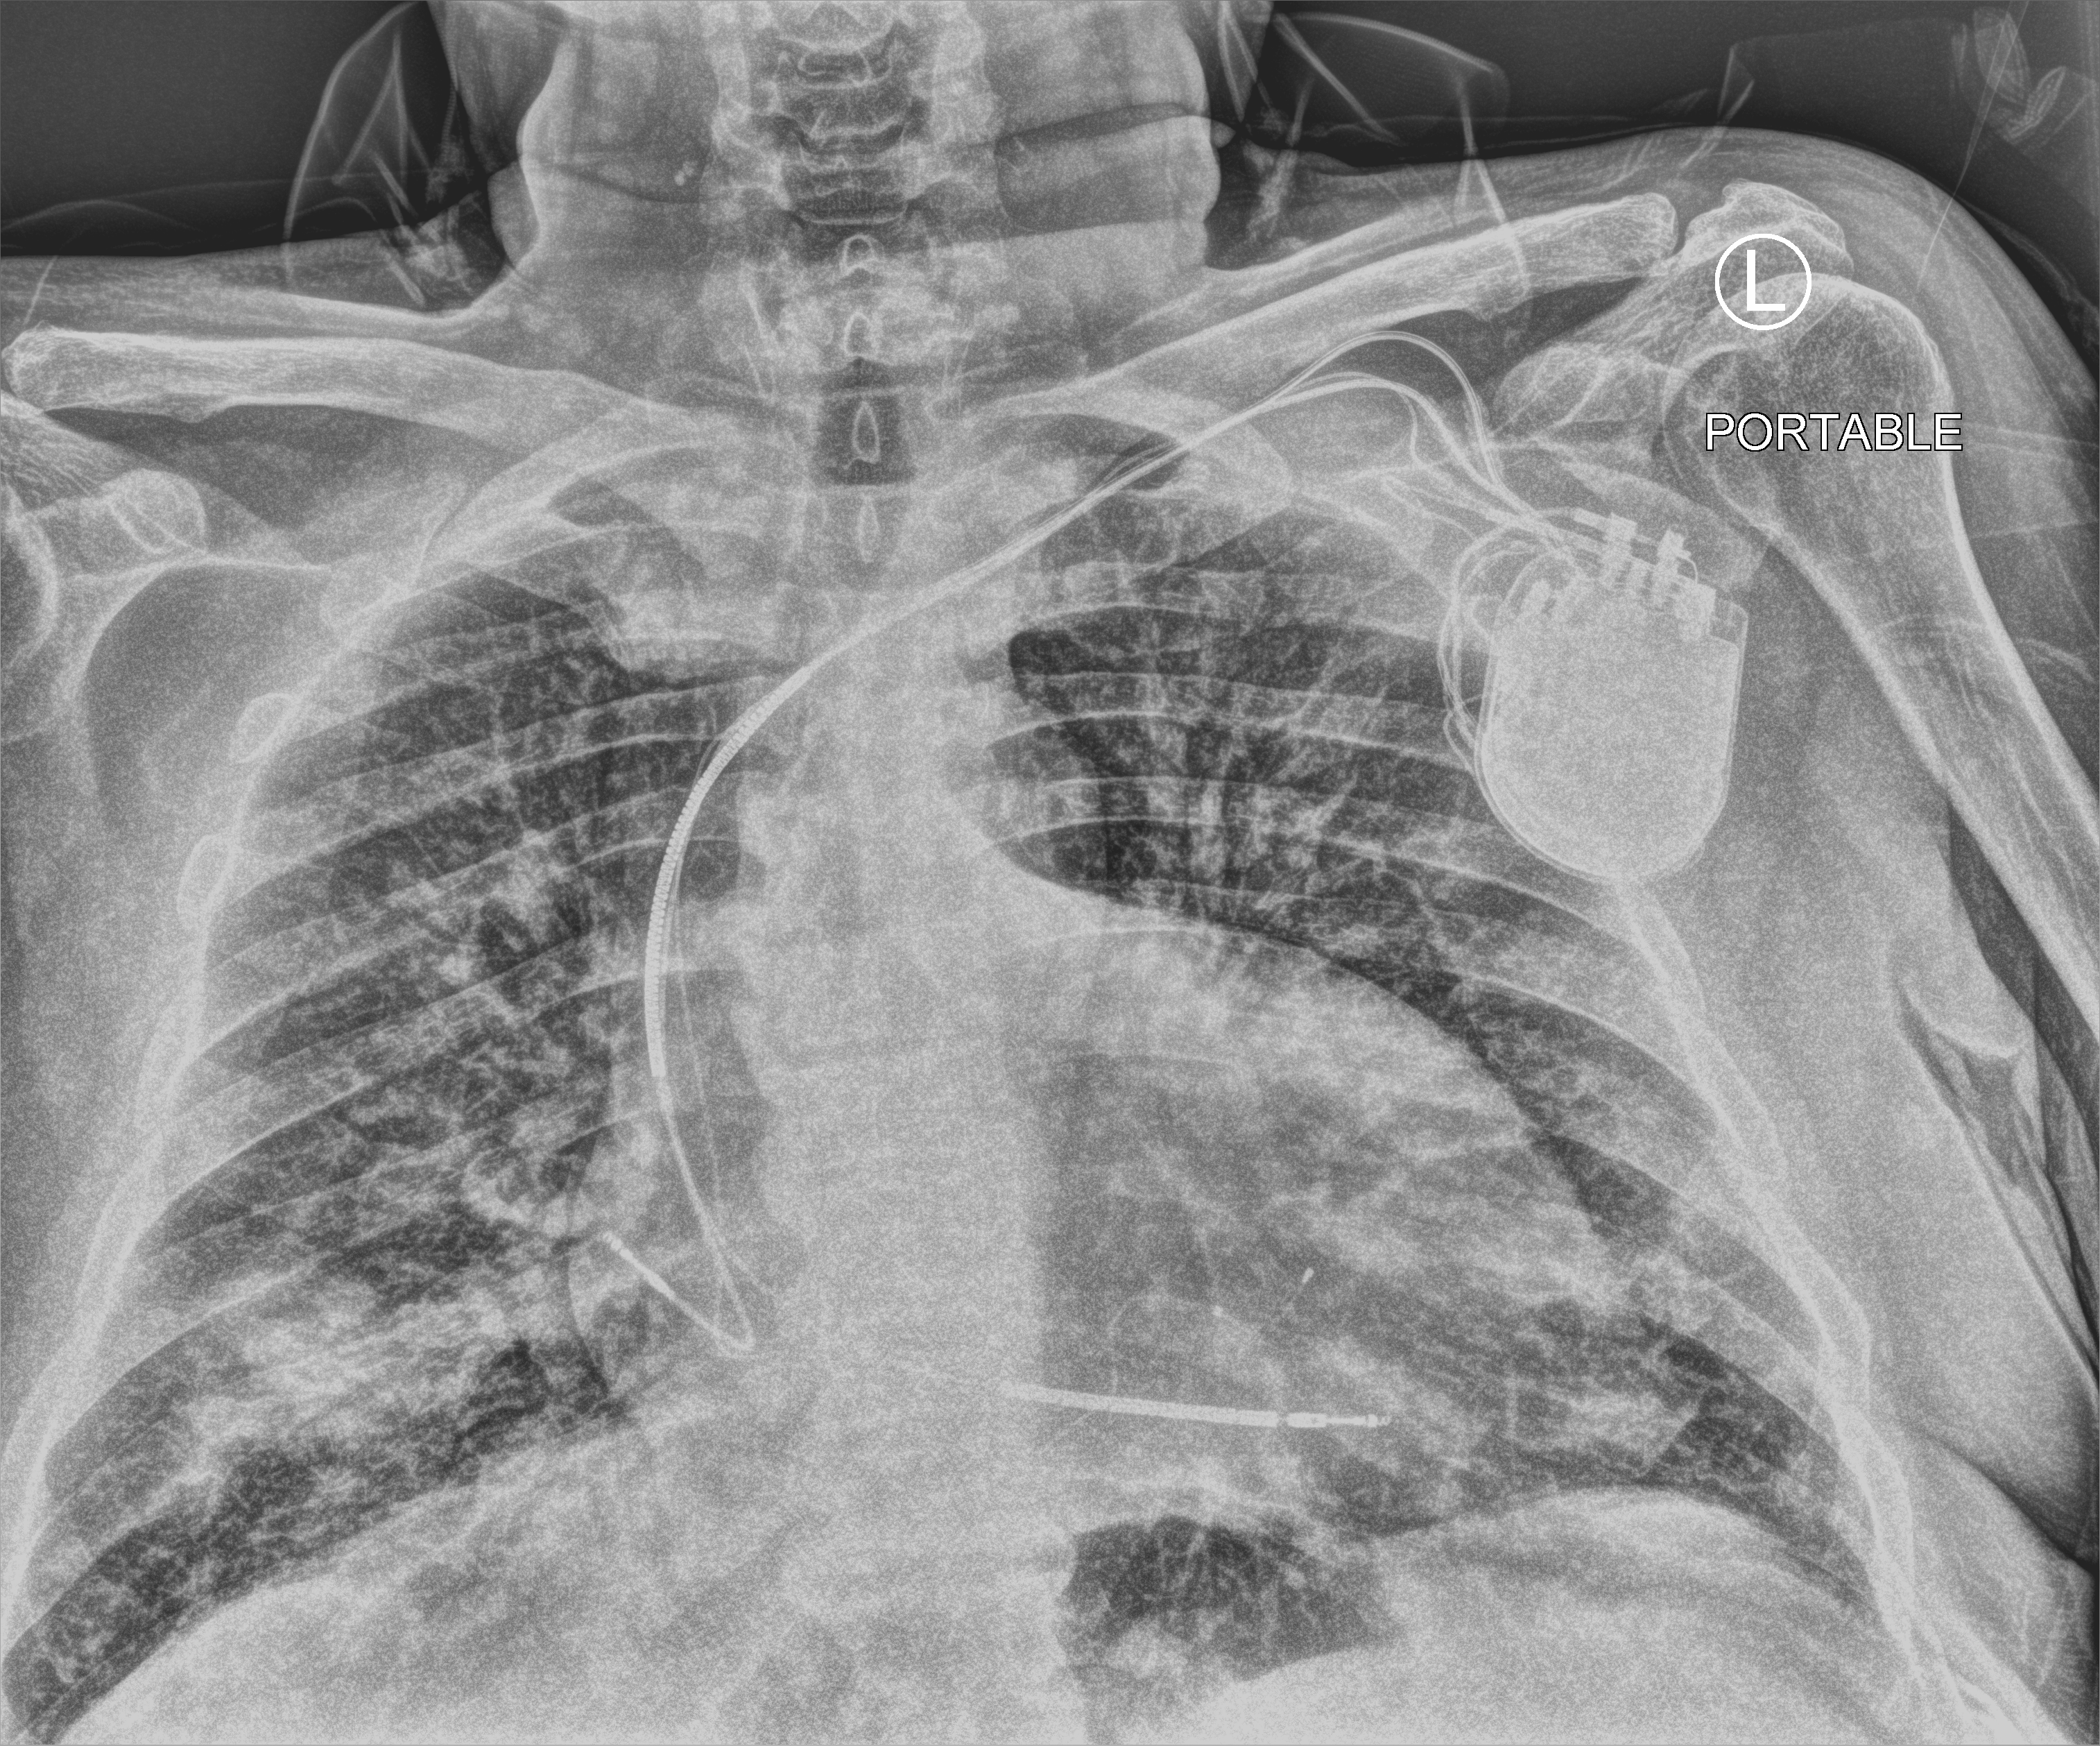
Bedside chest radiograph (computed radiography). Patient hospitalised with COVID-19; male, aged 60–74 years.
Hospital-stay facts (about this admission, not read from this image; timing relative to this image not recorded): length of hospital stay: 27 days; smoking status (admission record): former.